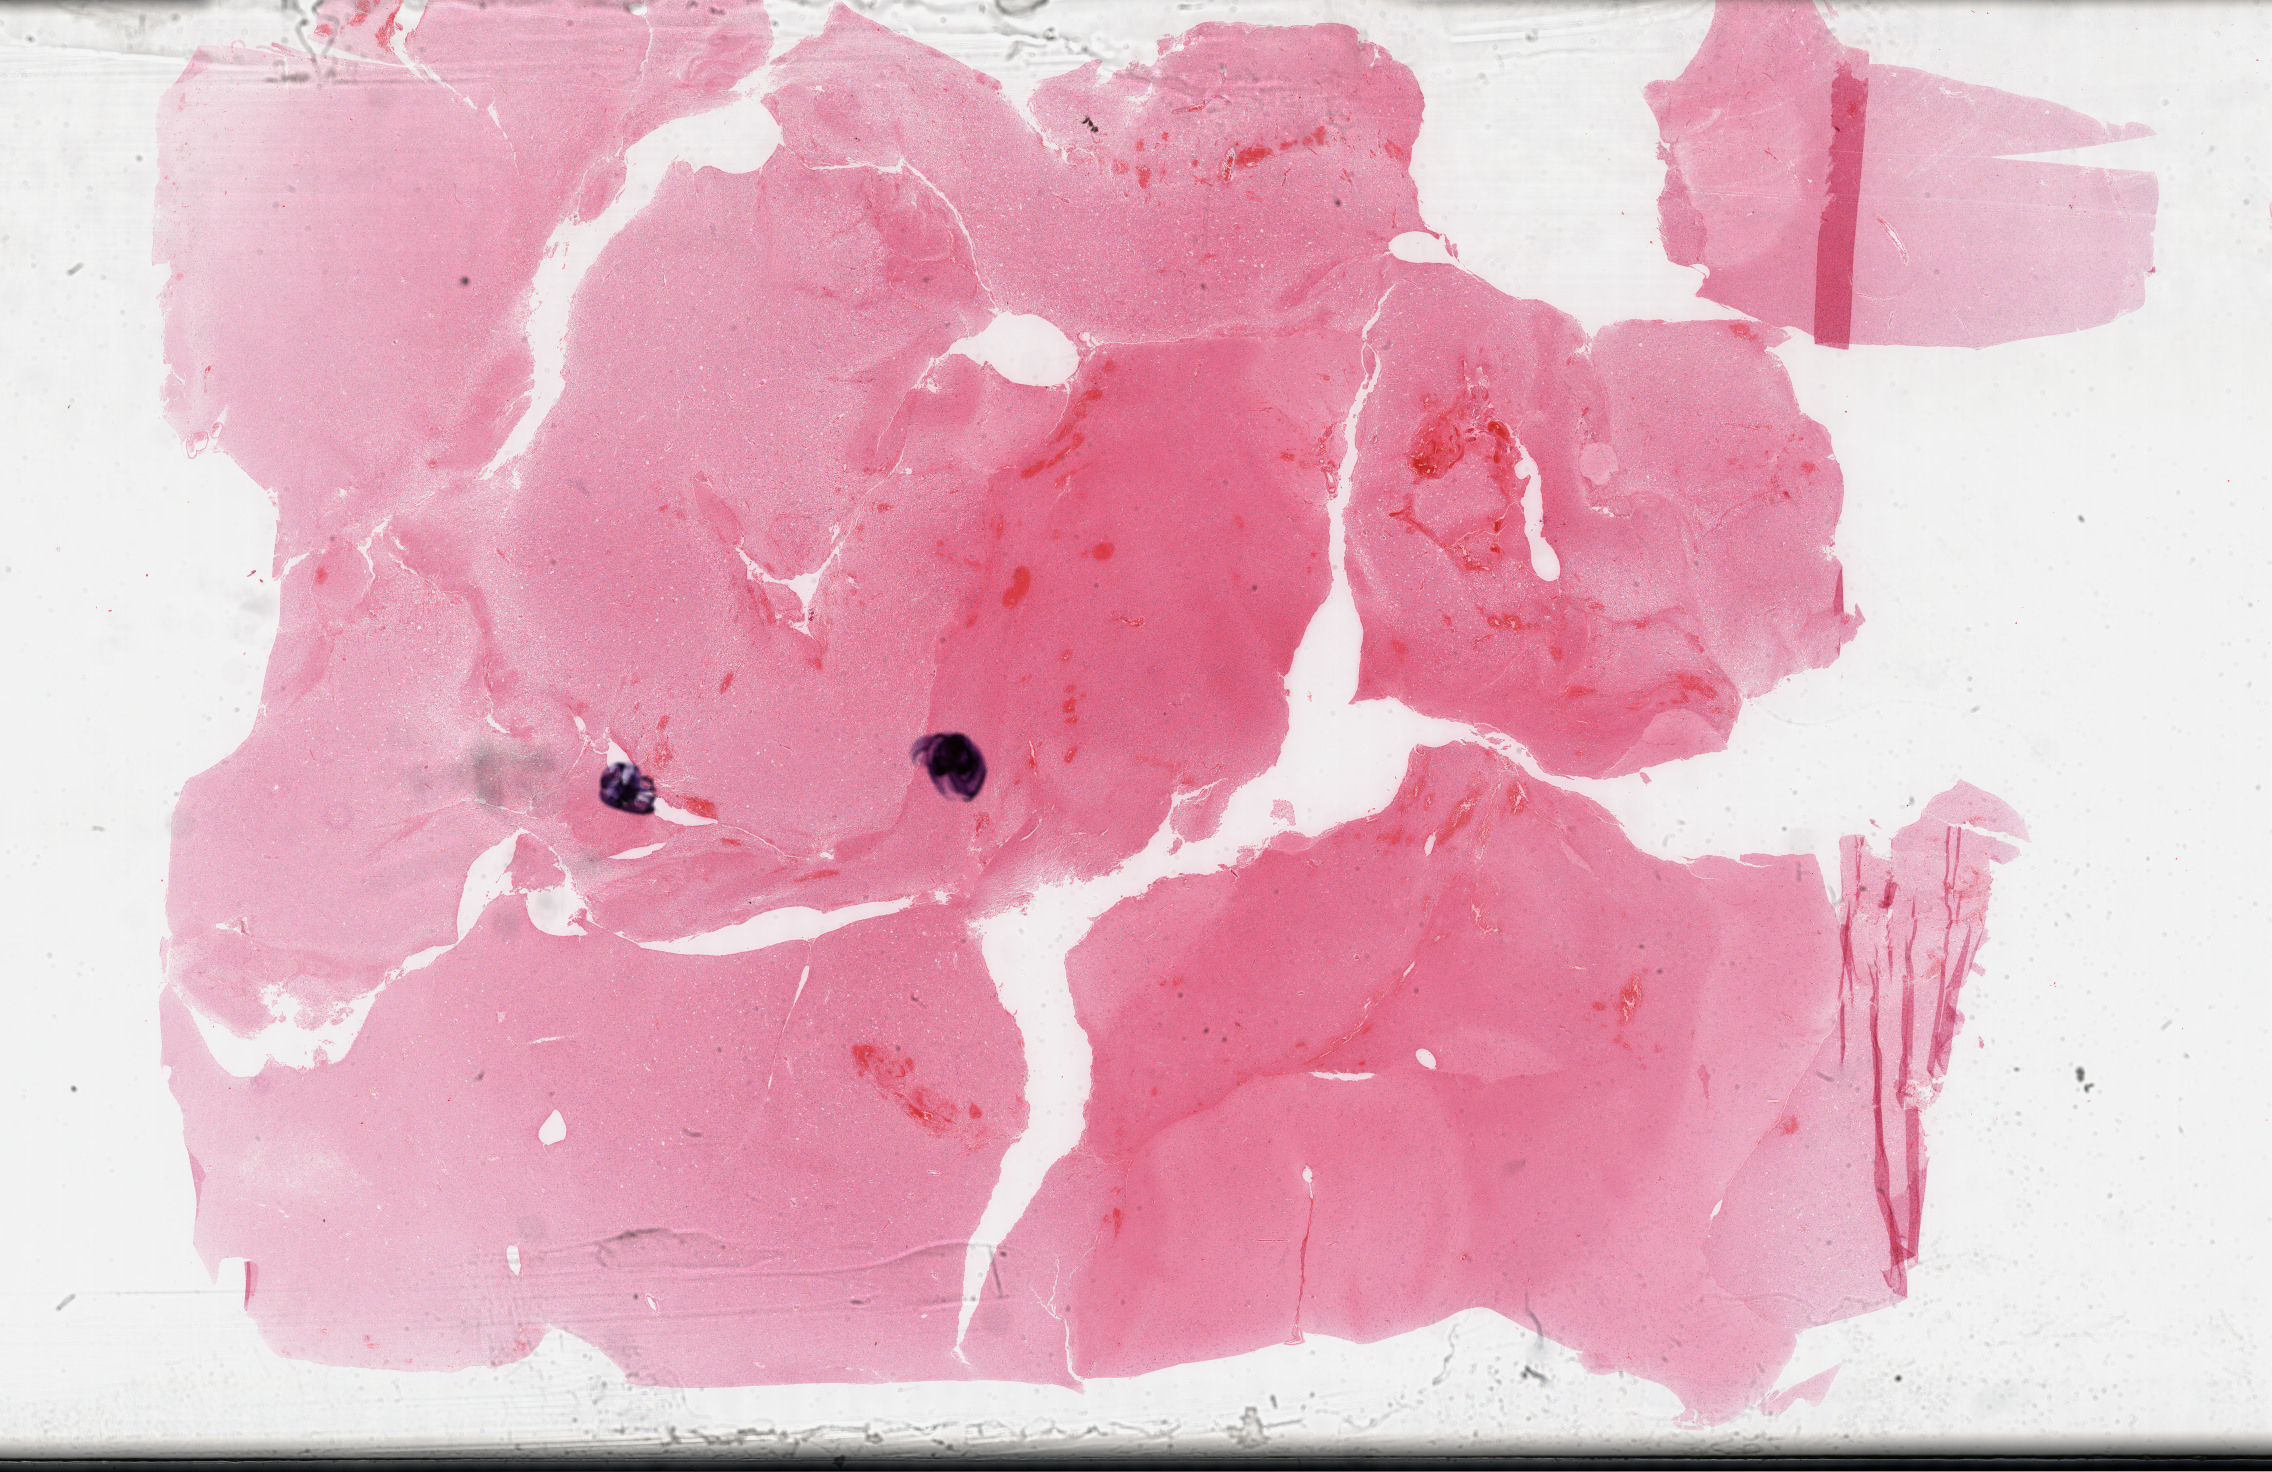
Whole-slide histology image, H&E-stained — whole scanned area (about 36.7 x 23.8 mm, acquisition: 40x scan) shown as a low-resolution overview, formalin-fixed paraffin-embedded (FFPE) diagnostic section, brain, primary tumour sample. Female, age 56 years at initial diagnosis. Histologic grade: G2 (moderately differentiated).
Diagnosis: Mixed glioma (cerebrum).